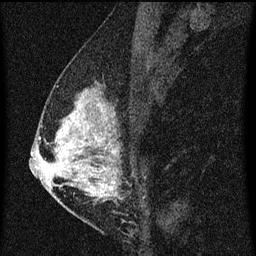
Breast MRI (dynamic contrast-enhanced), one sagittal slice; slice 27 of 60 in the series (ordered by position); dynamic contrast-enhanced series, image 2 of 3 at this slice position (ordered by acquisition); 1.5 T; TE 4.2 ms, TR 8 ms; 256 × 256 image matrix. Female patient, age 47 years.
Outlined on this slice (semi-automatic segmentation, software-assisted and operator-edited):
- analysis volume of interest (the breast-tissue region the enhancement analysis was run in; not a lesion): bounding box (x1, y1, x2, y2) in pixels: (50, 80, 138, 203)
- tumour enhancement mask (voxels above the 70 % enhancement threshold inside the analysis volume of interest): (50, 104, 117, 201)